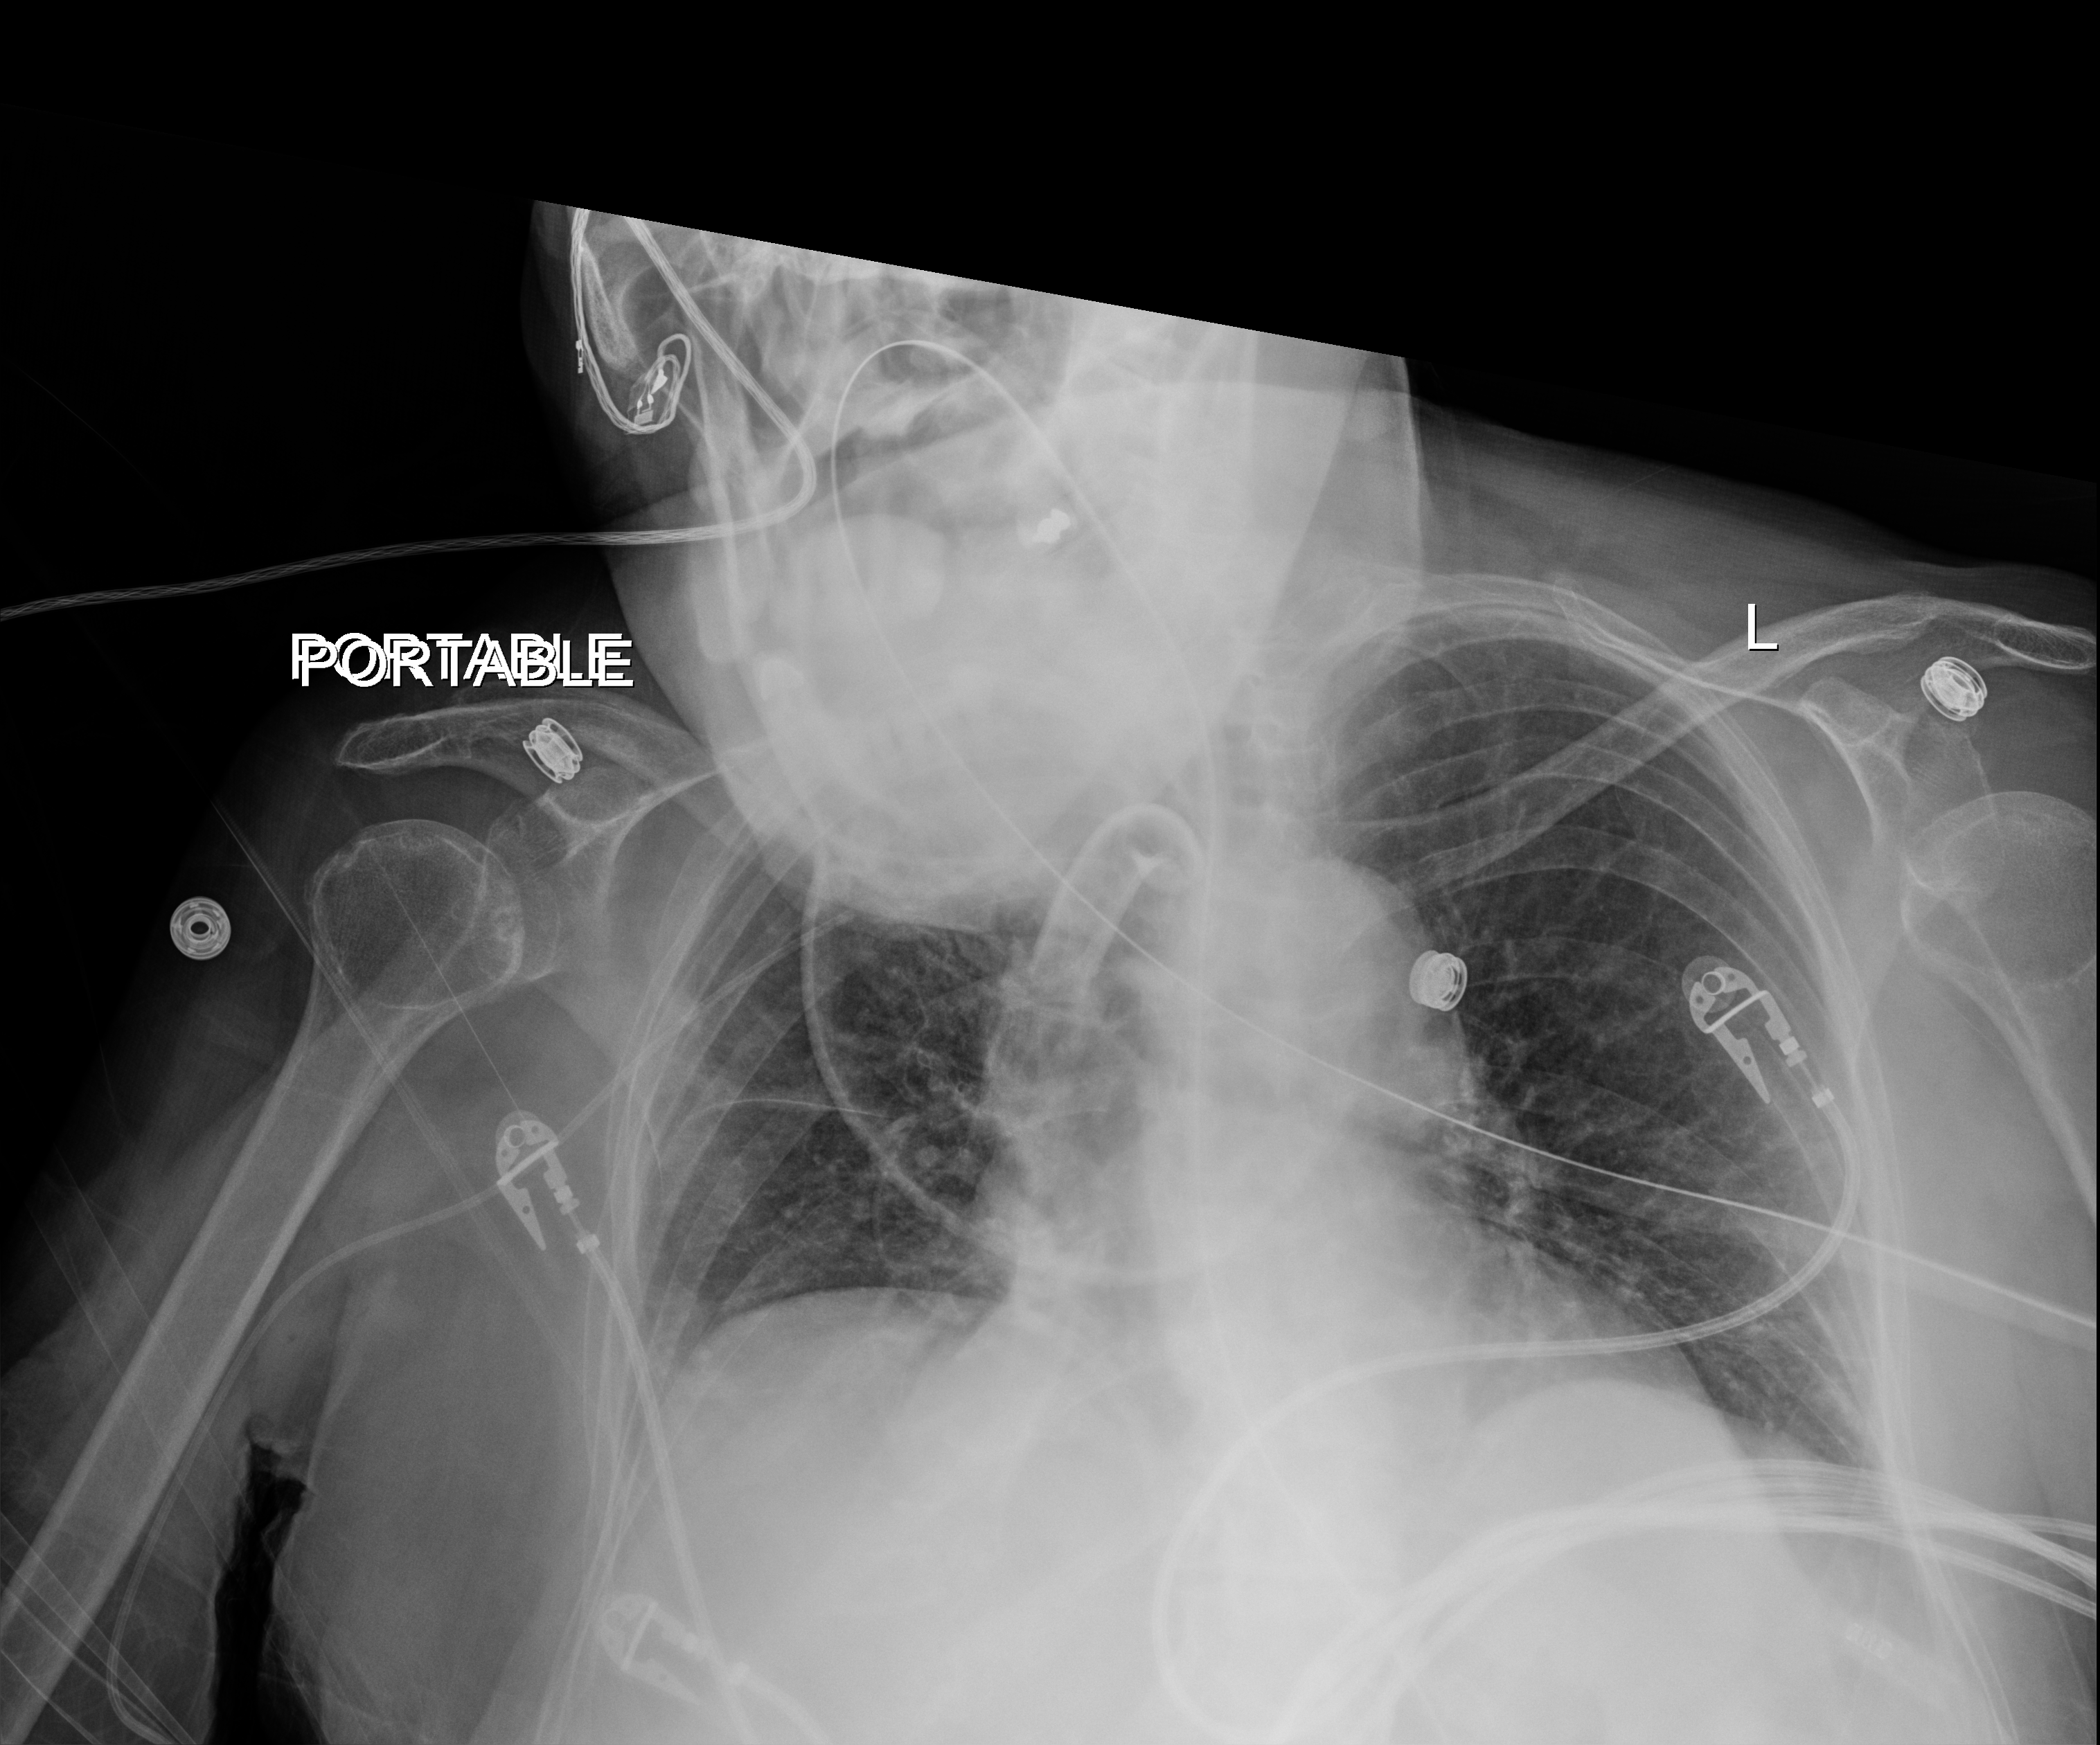
Bedside chest radiograph (digital radiography); anteroposterior (AP) projection. Female patient hospitalised with COVID-19, age 75–90 years.
Admission-level facts for this patient (not findings on this image; timing relative to this image not recorded):
- chronic kidney disease (admission record): yes